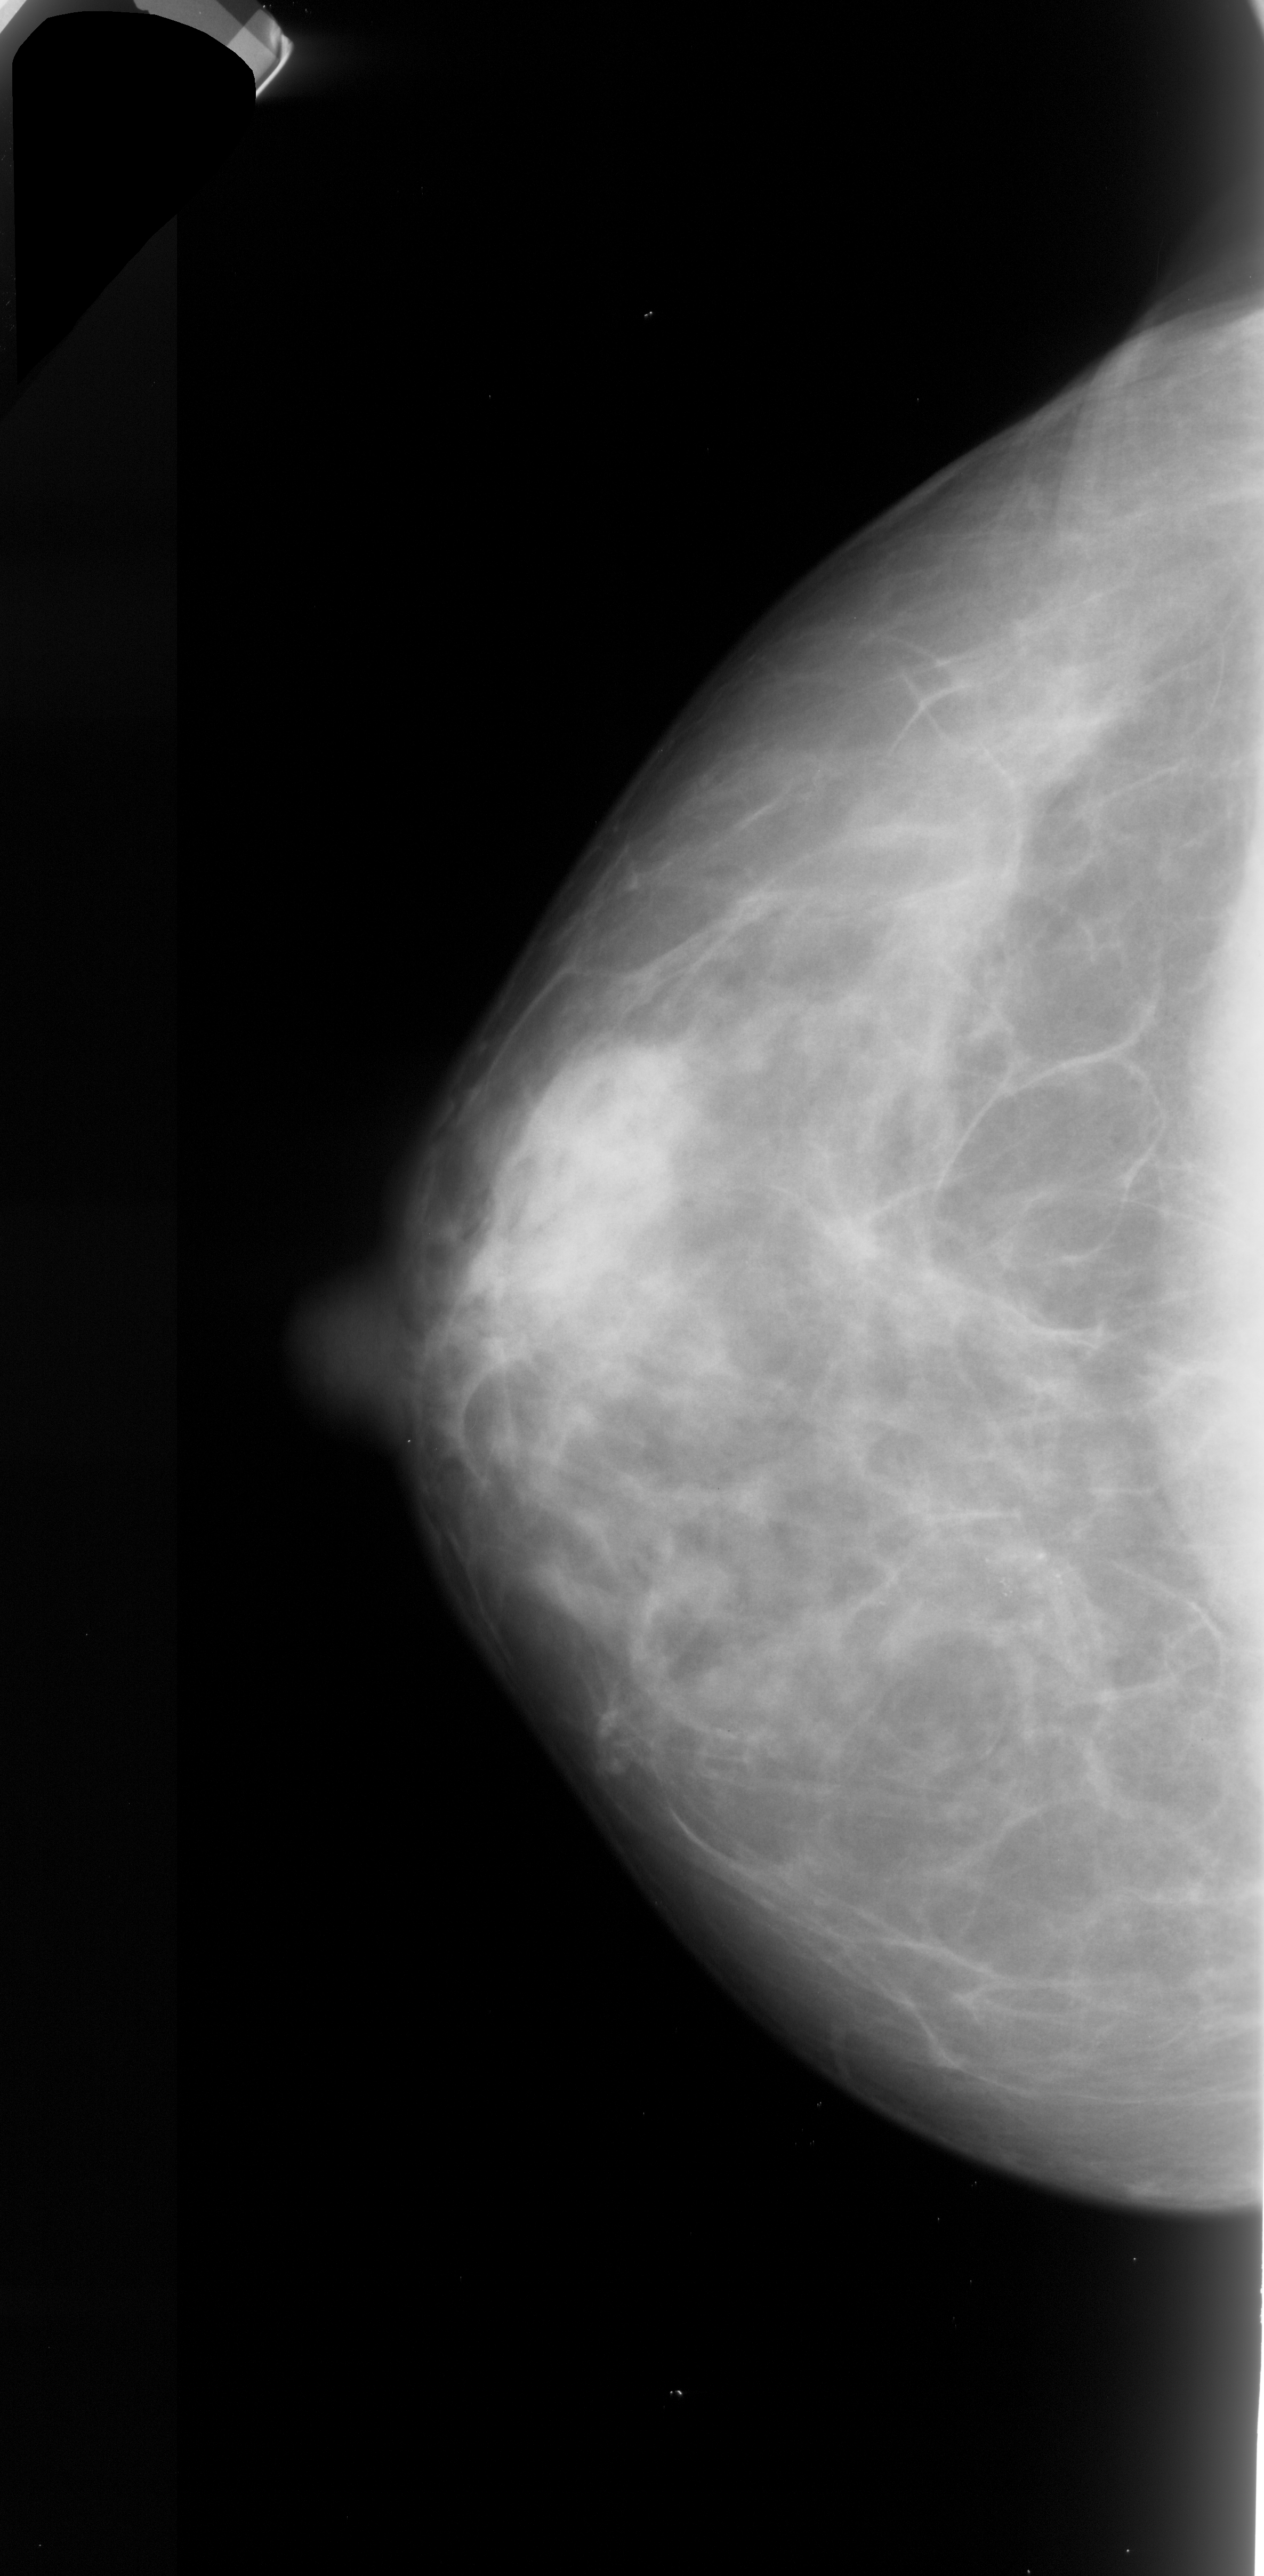
Digitized screen-film mammogram; left breast; CC view; BI-RADS breast density category 1 (scale 1–4).
- Radiologist-marked abnormalities on this image: calcifications, morphology pleomorphic, distribution clustered; BI-RADS assessment category 4; pathology (as recorded): malignant.